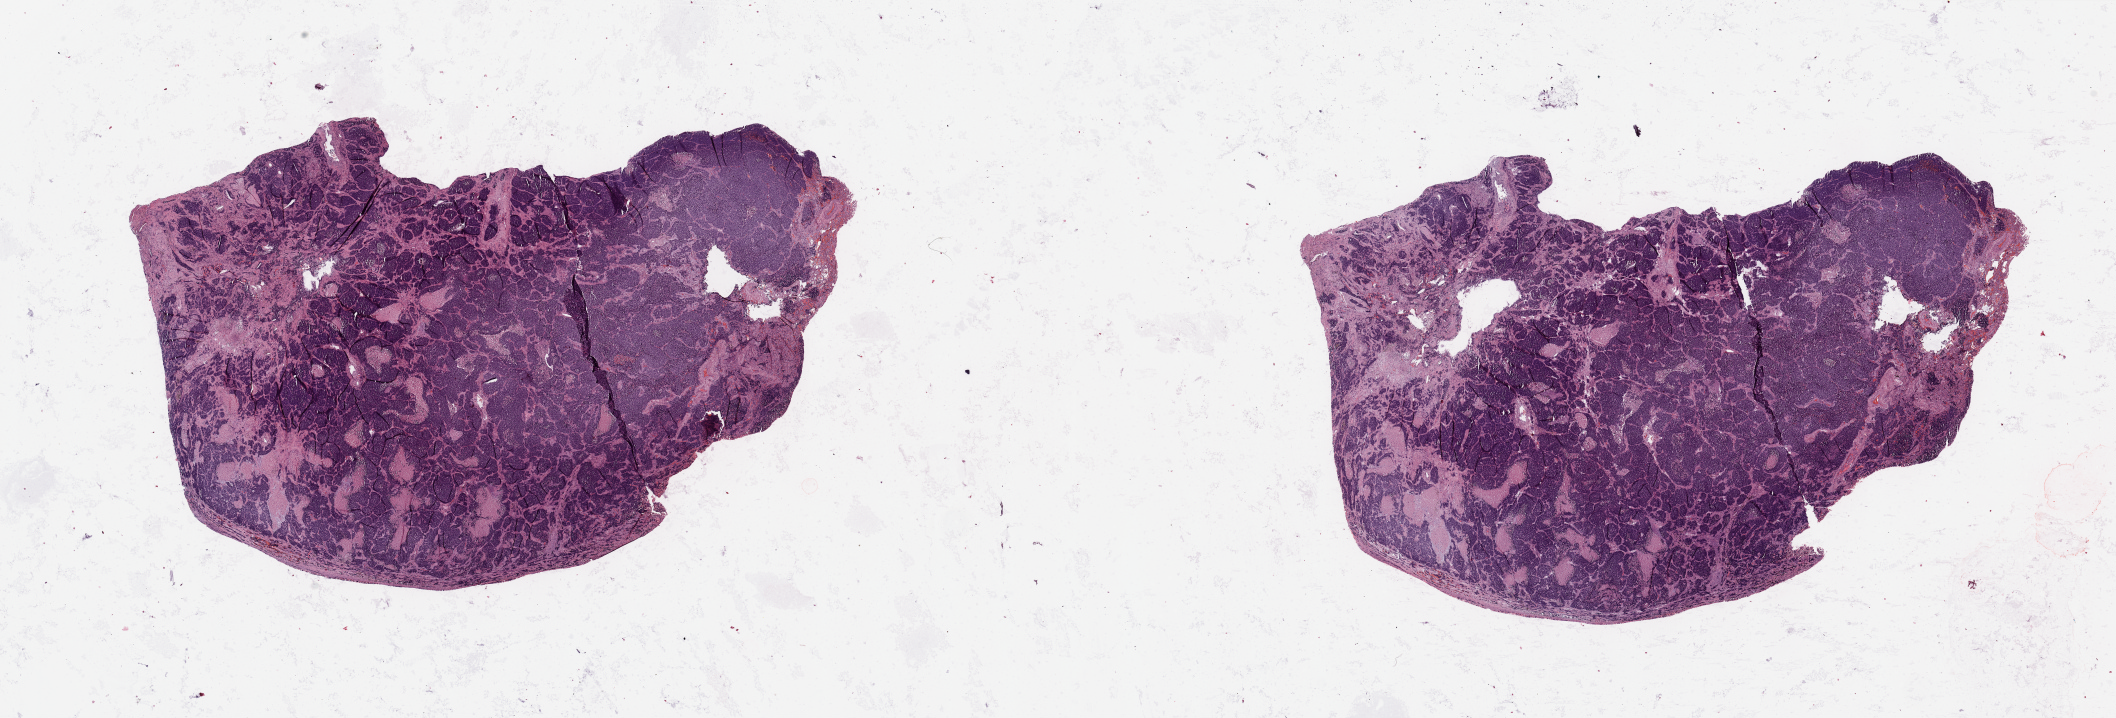
Digitized H&E tissue section (whole slide) — low-resolution overview of the scanned area, about 33.5 x 11.4 mm (acquisition: 20x scan). Tumour tissue sample, lung. 63-year-old male patient.
Primary tumour site (as recorded): left upper lobe. Patient diagnosis (cohort enrolment): squamous cell carcinoma (lung).